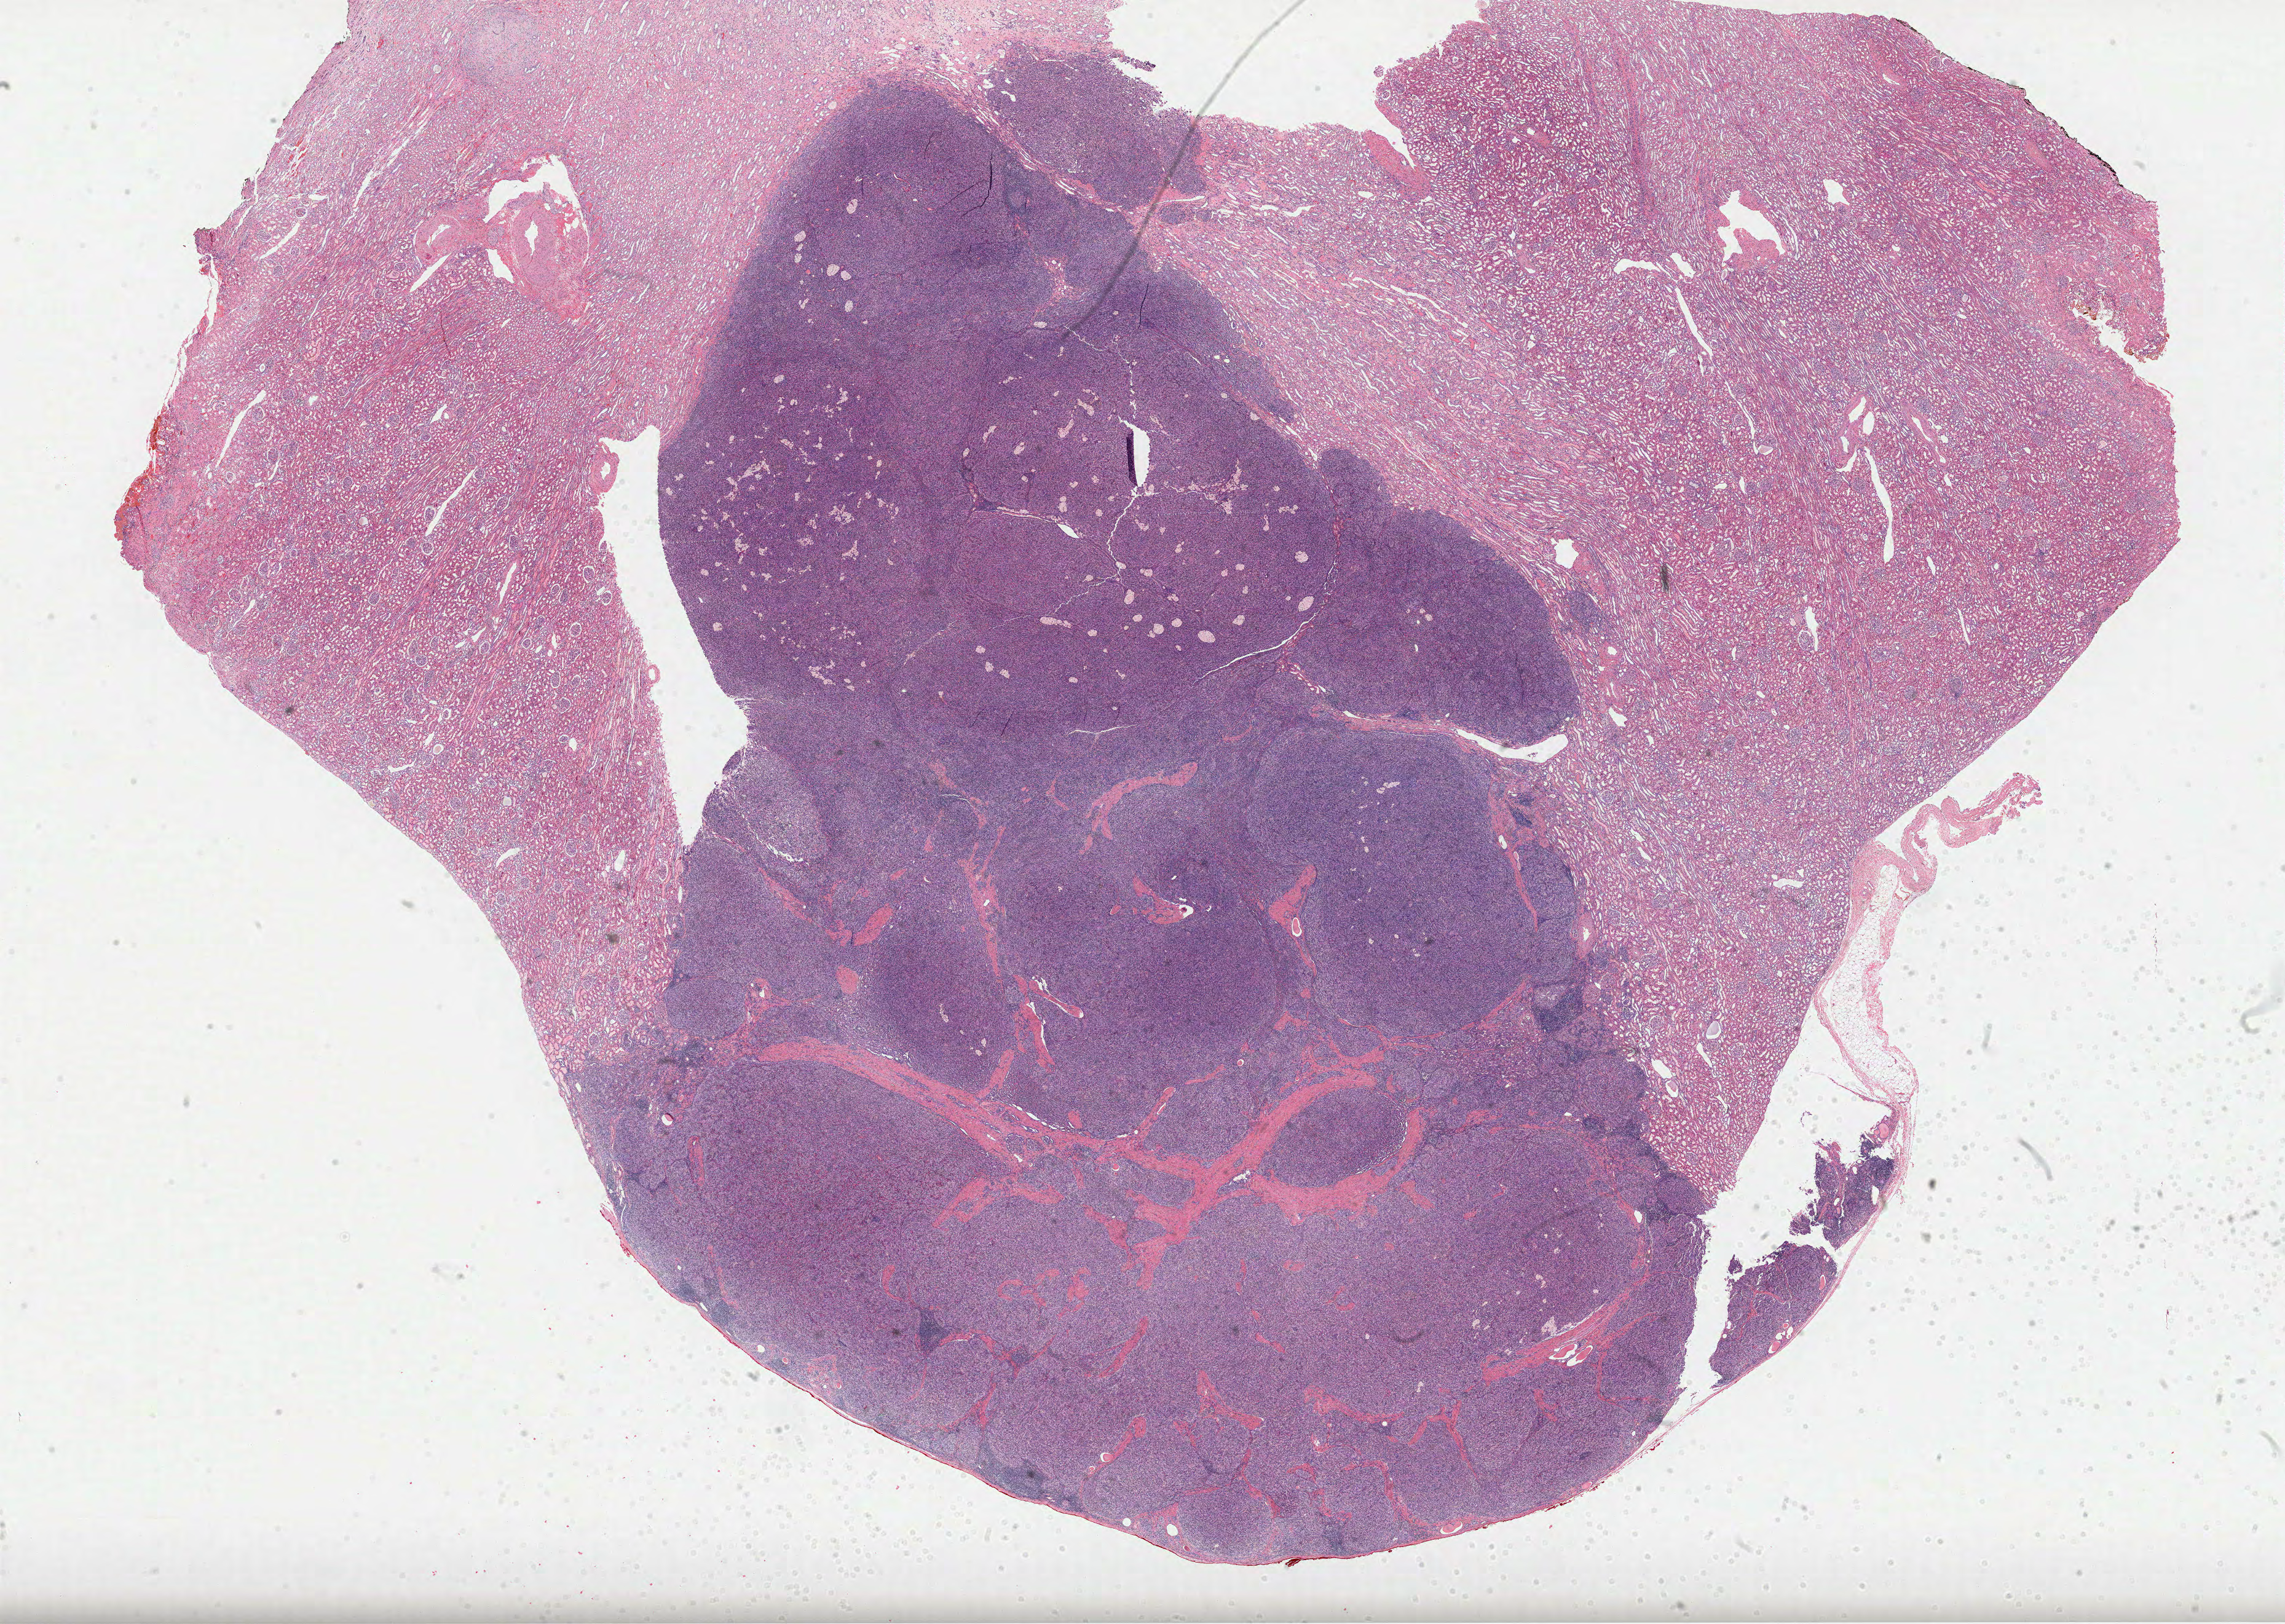
Hematoxylin and eosin (H&E) stained whole-slide image, whole scanned area (about 30.0 x 21.3 mm) shown as a low-resolution overview, FFPE section, sample: primary tumour, kidney. Female, age 47 years at initial diagnosis.
- TNM: T1 NX M0
- pathologic diagnosis: Papillary adenocarcinoma, NOS
- AJCC pathologic stage: I